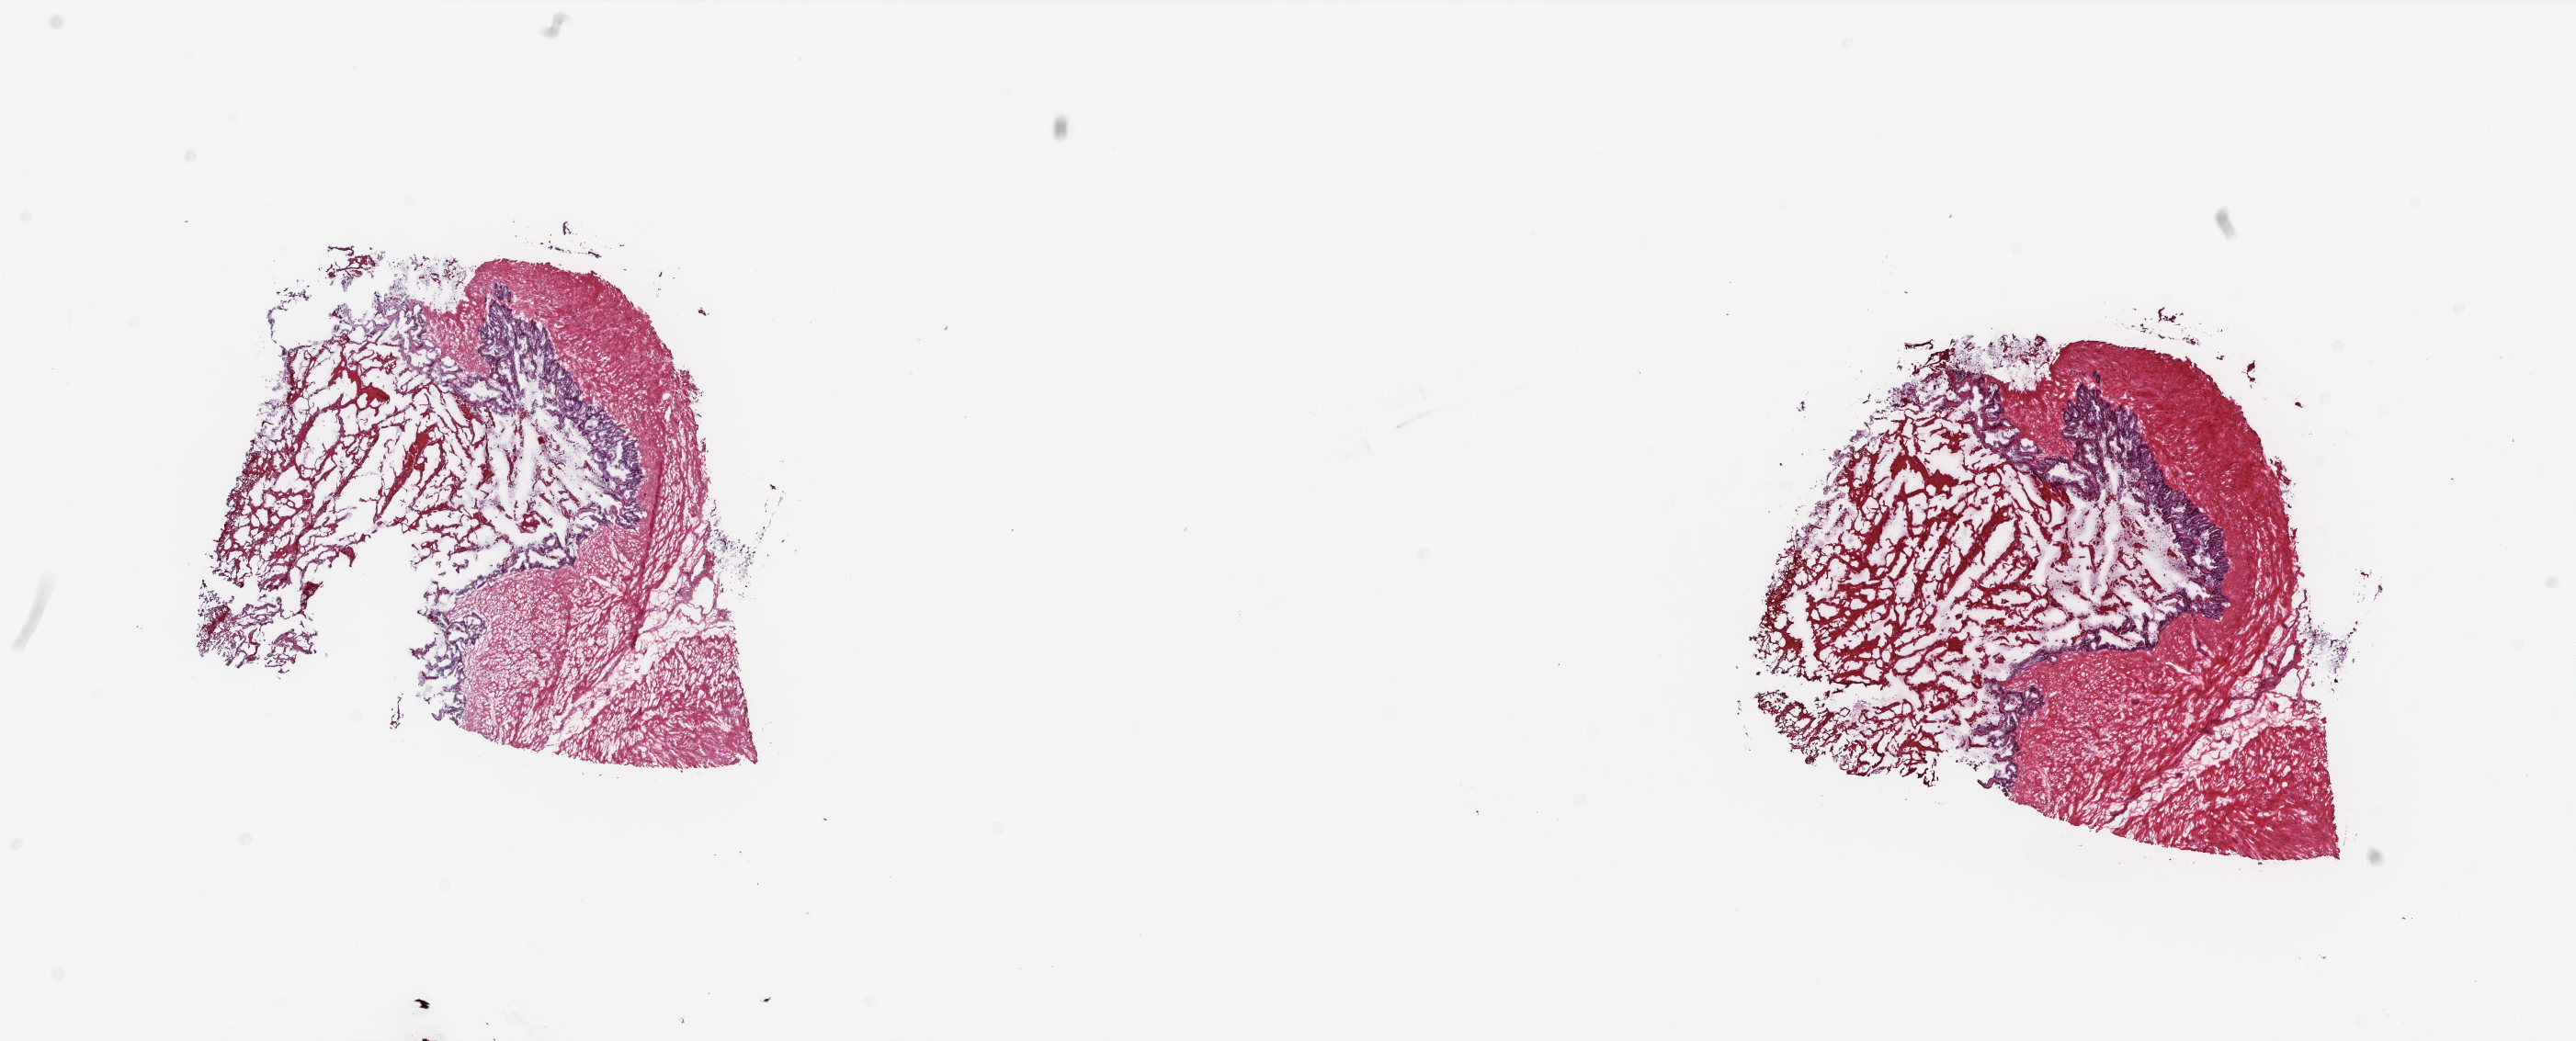
Whole-slide histology image, H&E-stained — shown as a low-resolution overview of the whole scanned area (about 22.6 x 9.1 mm), frozen section from the top of the tissue portion, prostate, solid tissue normal (non-tumour tissue) sample. Male, age 50 years at initial diagnosis. Composition of this section per pathologist review: tumour cells 0%, tumour nuclei 0%, normal cells 30%, stromal cells 70%, necrosis 0%. Infiltration values recorded for this section: lymphocyte infiltration 40%, monocyte infiltration 20%, neutrophil infiltration 20%.
* this section: solid tissue normal (non-tumour) sample from the same patient
* patient diagnosis: Adenocarcinoma, NOS